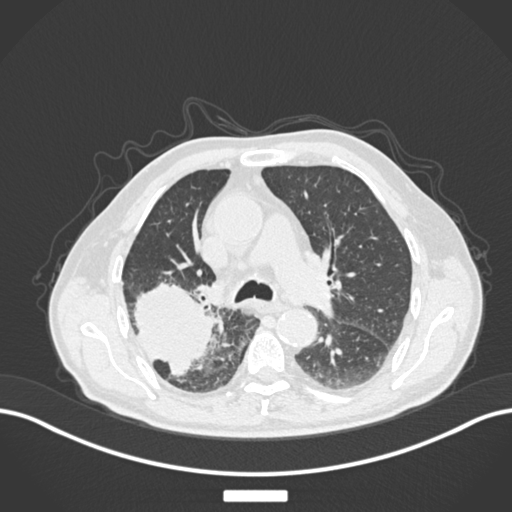
Chest CT, one axial slice. Slice 112 of 201 in the series (ordered by position). Reconstruction kernel B30f. Lung window (W 1500 / L -600 HU). 1 mm slice thickness. 512 × 512 image matrix, field of view 400 × 400 mm. Patient: male, 72 years. From the clinical record (not read from this slice): clinical TNM (as recorded): T3 N2 M0.
Outlined on this slice (bounding box drawn by a radiologist):
- lung tumour (recorded histology: adenocarcinoma): bounding box (x1, y1, x2, y2) in pixels: (132, 269, 218, 378)